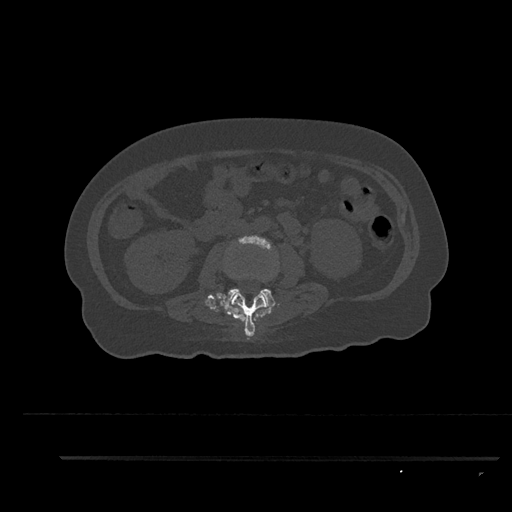
CT including the spine, one axial slice. Slice 123 of 797 in the series (ordered by position). Reconstruction kernel Br40s/3. Bone window (W 1800 / L 400 HU). 0.5 mm slice thickness. 512 × 512 image matrix, field of view 408 × 408 mm. Female patient, age 44 years. Case-level facts recorded for this patient, not image findings: primary cancer: renal; vertebrae with lytic lesions (as recorded): L1.
Structures marked on this image (semi-automatic segmentation, software-assisted and operator-edited):
- L2 vertebra: bounding box <226,292,269,337> (left, top, right, bottom; pixels)
- L3 vertebra: <223,235,279,307>